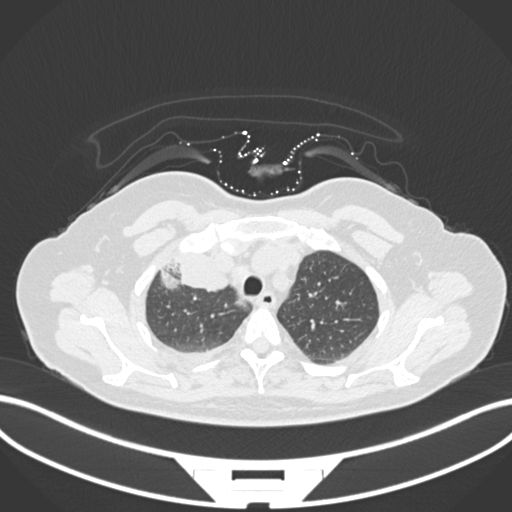
Chest CT, one axial slice. Slice 134 of 172 in the series (ordered by position). Lung window (W 1500 / L -600 HU). 512 × 512 image matrix, field of view 400 × 400 mm. Female patient, age 52 years. Case-level facts recorded for this patient, not image findings: clinical TNM (as recorded): T3 N1 M1.
Annotated regions visible in this slice (rectangle marked by the reading radiologist):
- lung tumour (recorded histology: adenocarcinoma): bounding box <163,250,233,296> (left, top, right, bottom; pixels)